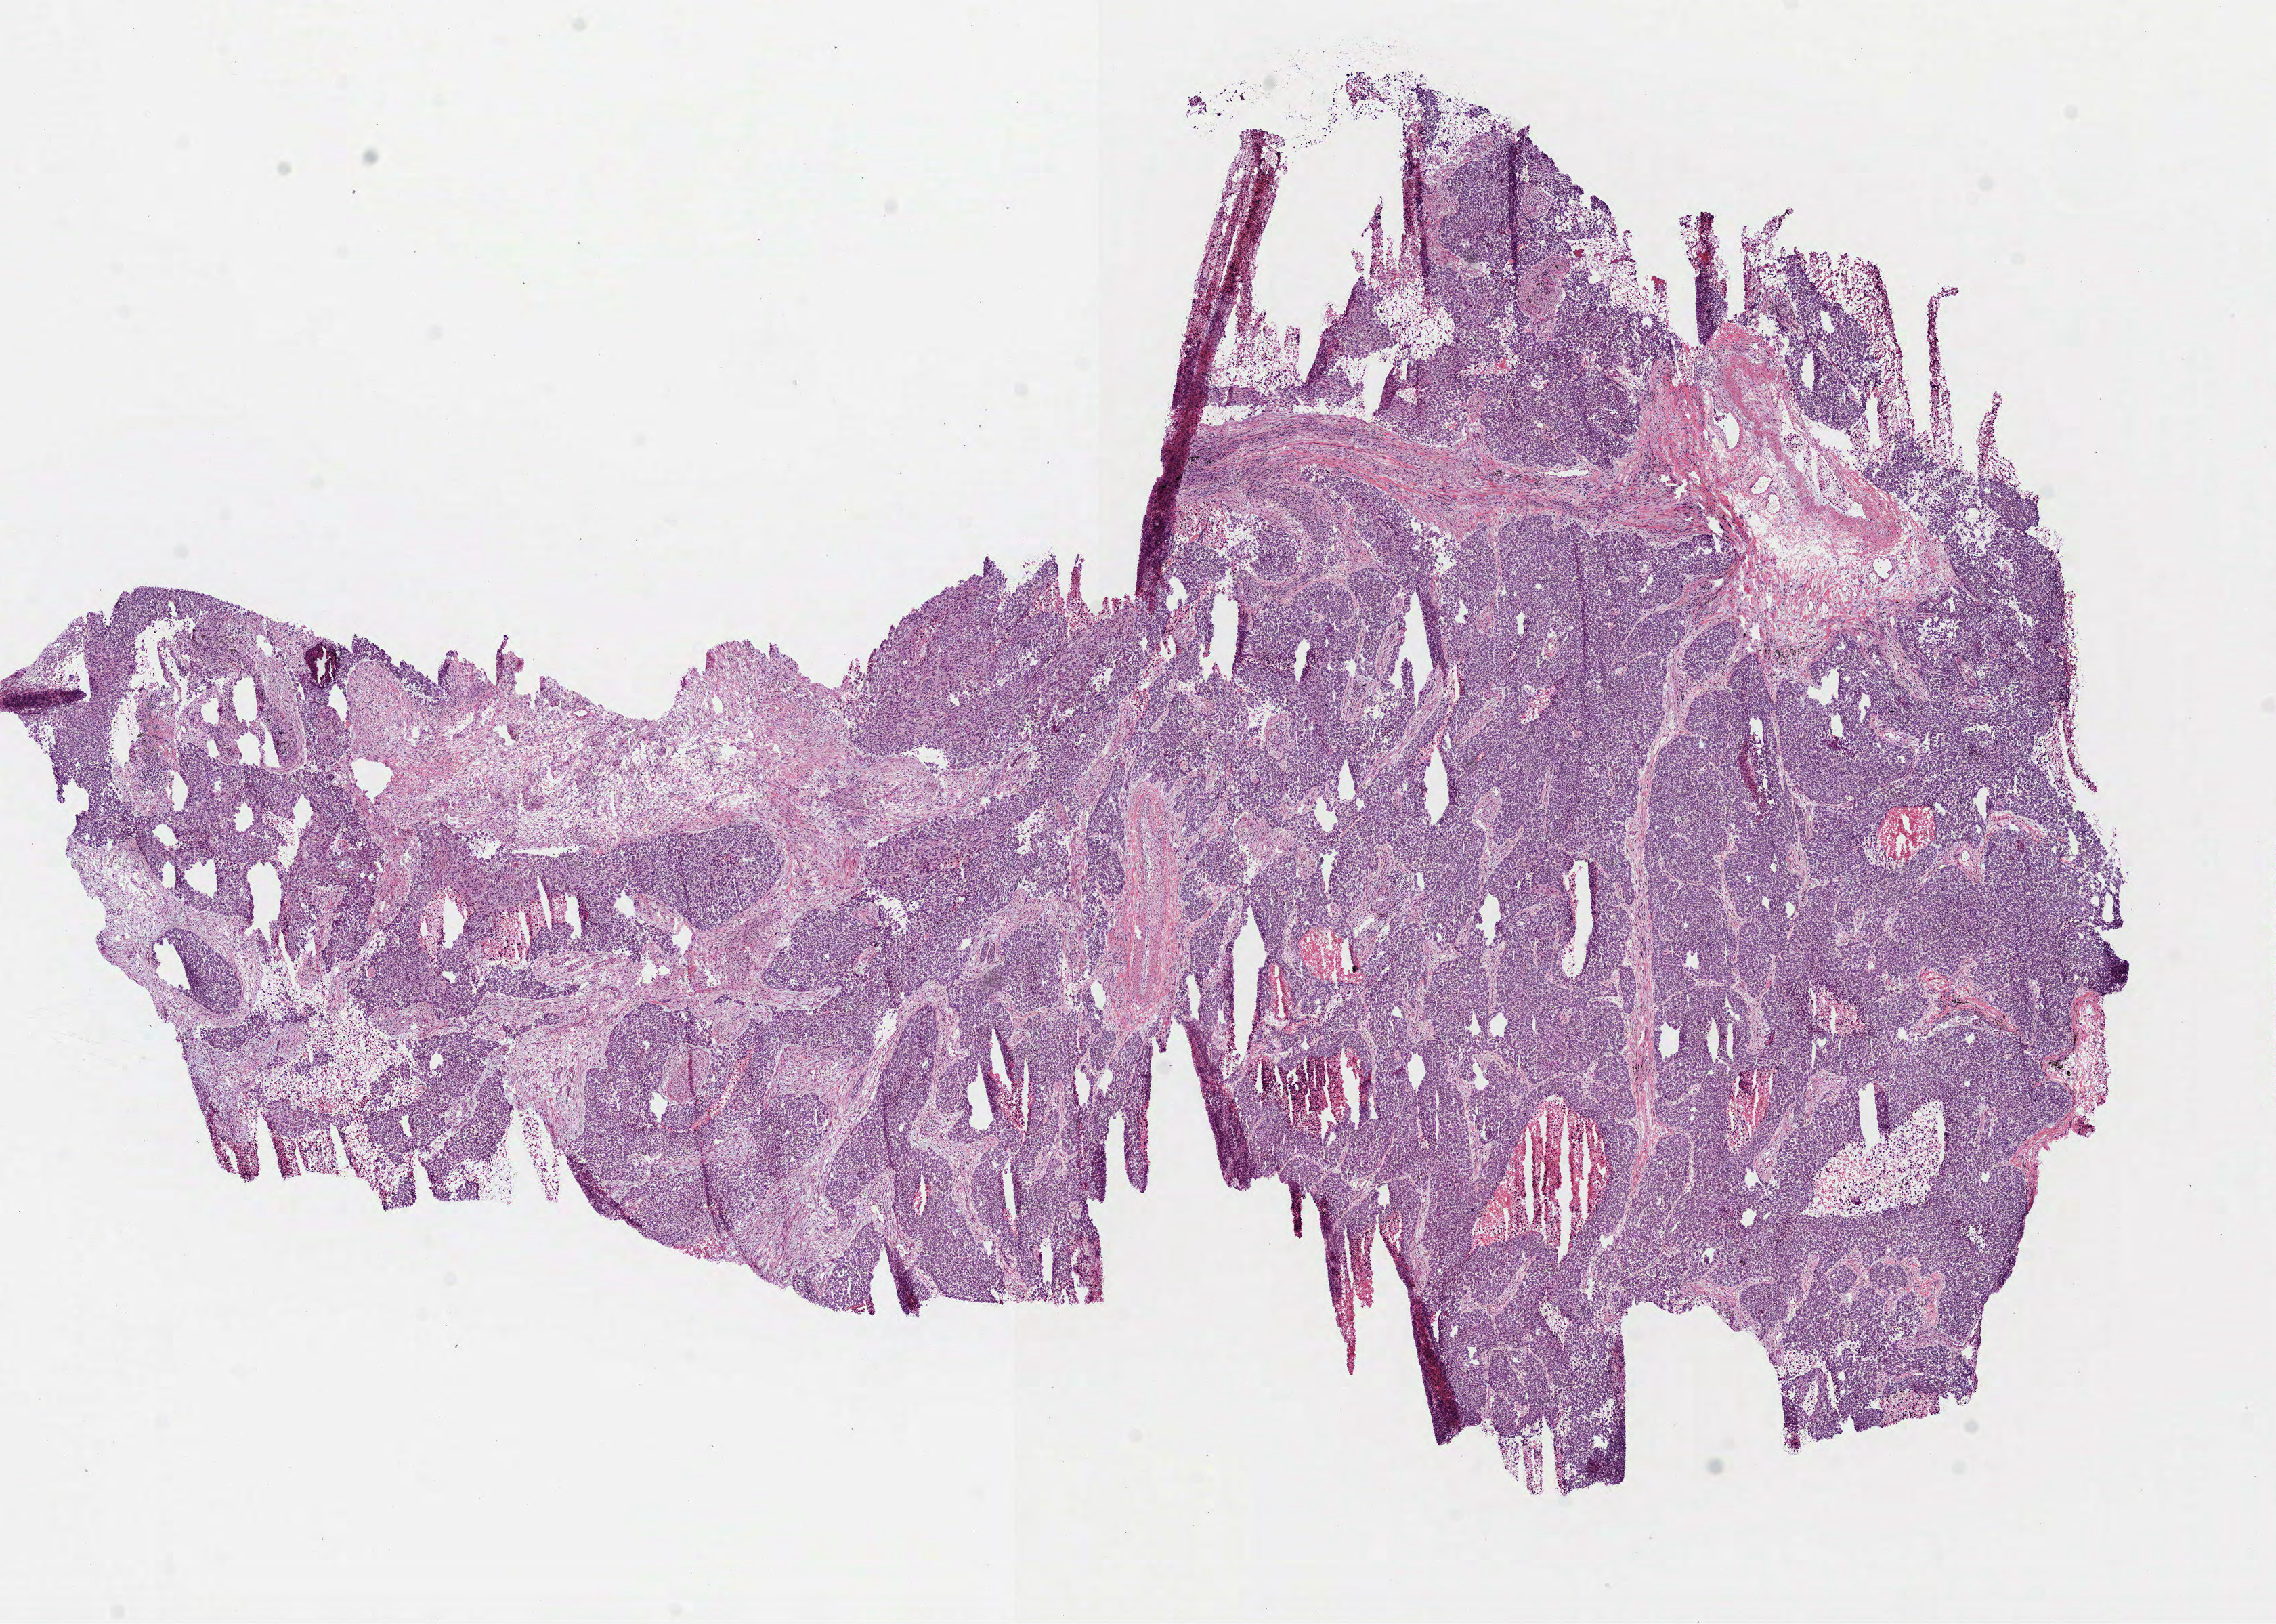
Digitized H&E tissue section (whole slide), a low-resolution overview of the entire scanned area, about 13.6 x 9.7 mm (acquisition: 40x scan), frozen section from the bottom of the tissue portion, lung, primary tumour sample. Male, age 70 years at initial diagnosis. Slide review estimates, as recorded: tumour cells 95%, tumour nuclei 90%, normal cells 0%, stromal cells 0%, necrosis 5%. Infiltration values recorded for this section: lymphocyte infiltration 2%, monocyte infiltration 1%, neutrophil infiltration 1%.
• AJCC pathologic stage: IB
• histologic diagnosis: Basaloid squamous cell carcinoma (lower lobe, lung)